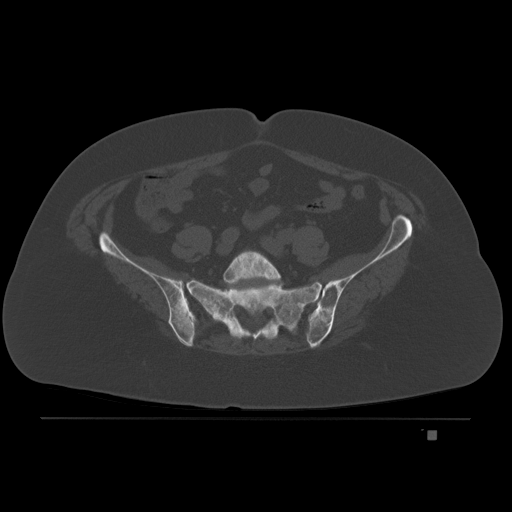
CT including the spine, one axial slice; position 25 of 221 along the scan axis; bone window (W 1800 / L 400 HU); 3 mm slice thickness; 512 × 512 image matrix. Patient: female, 63 years. Case-level facts recorded for this patient, not image findings: primary cancer: breast.
Structures marked on this image (semi-automatically segmented with operator editing):
- L5 vertebra: bounding box [x1, y1, x2, y2] px = [223, 249, 281, 286]